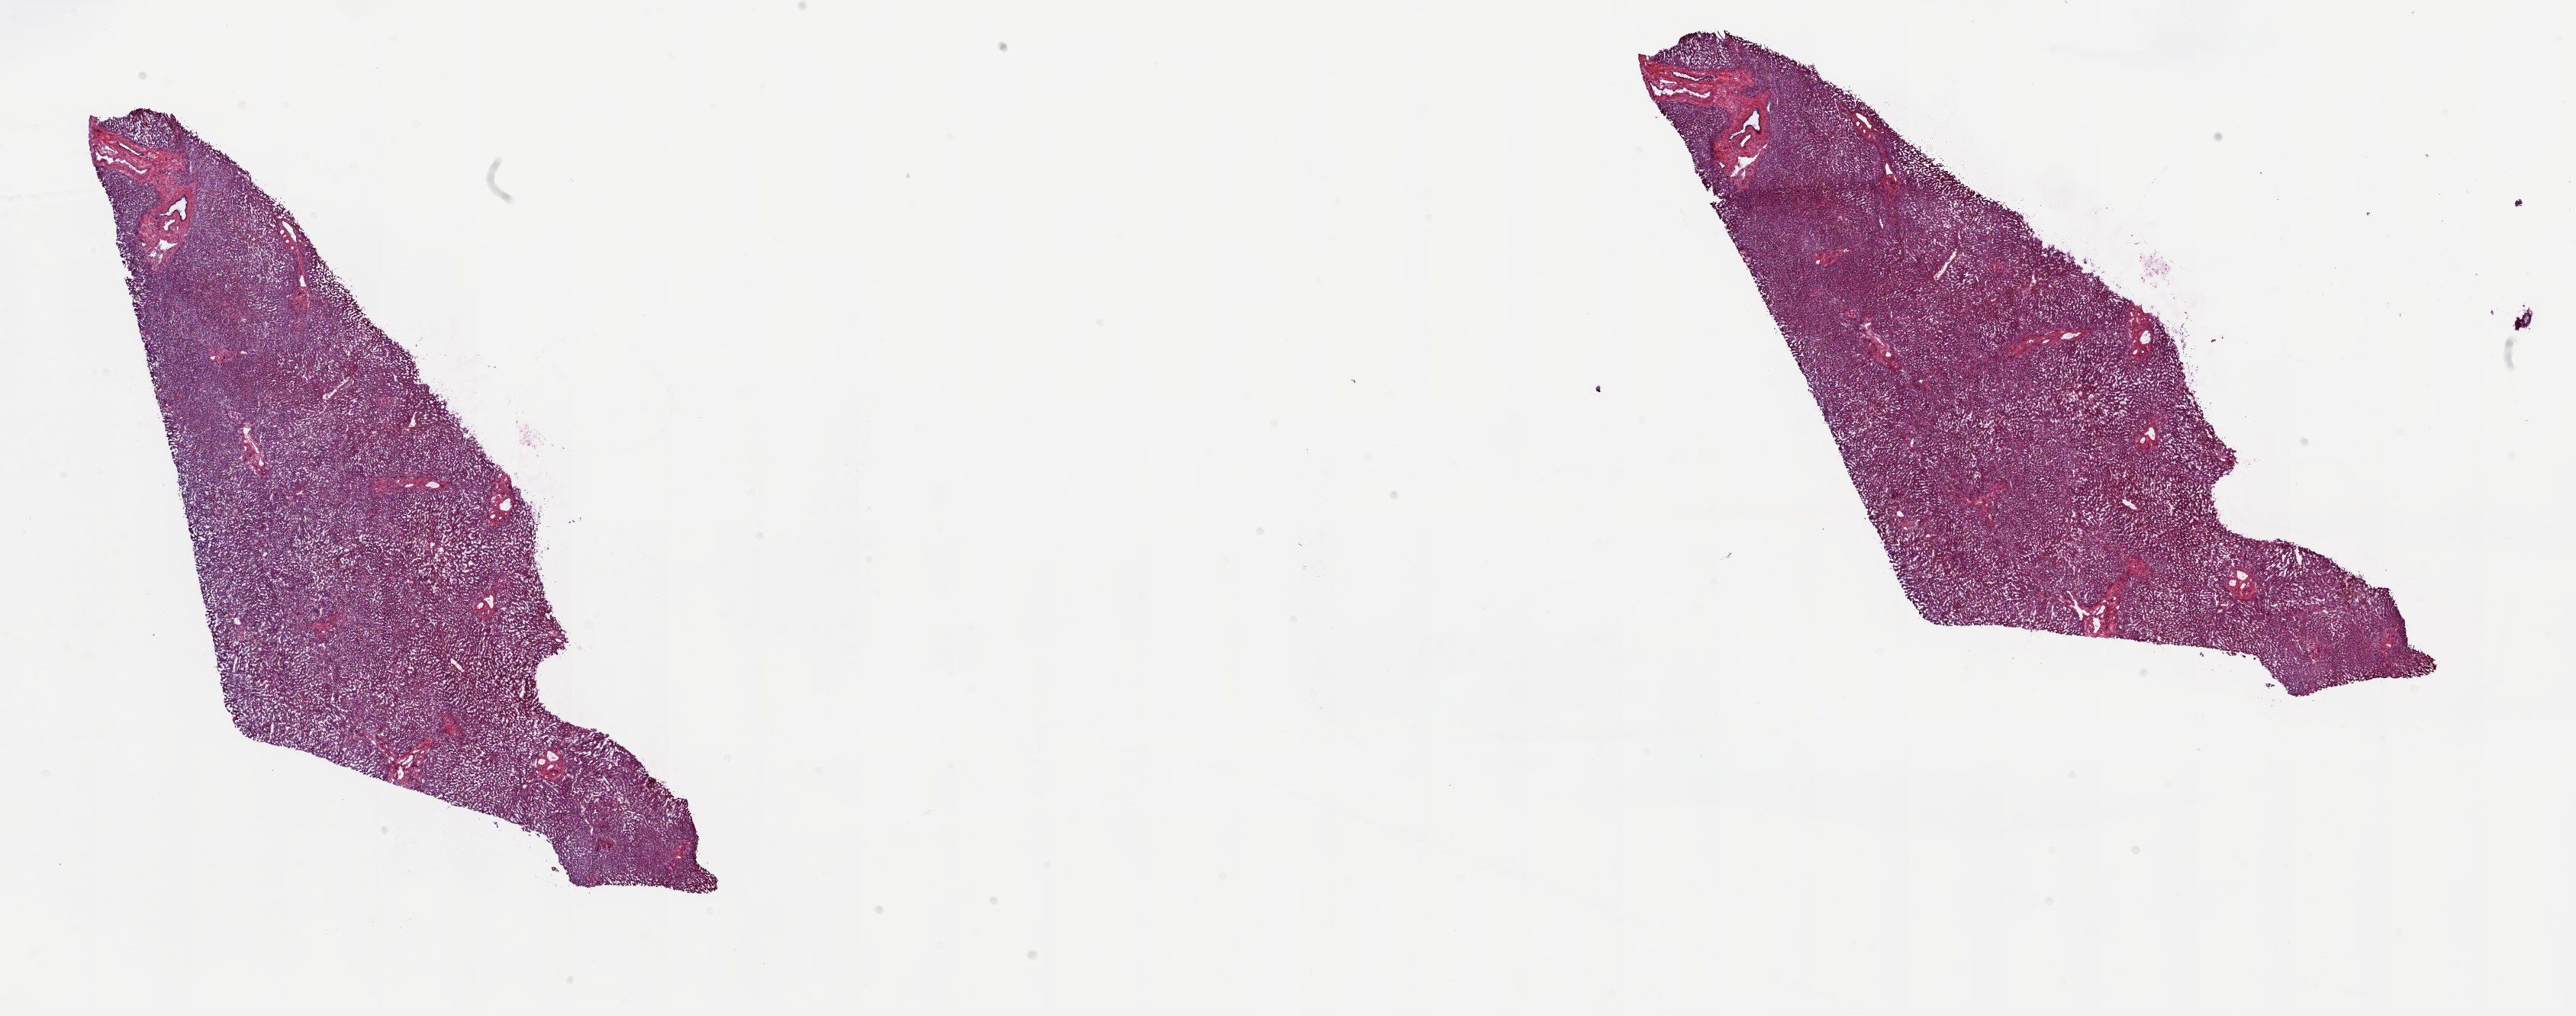
Digitized H&E tissue section (whole slide), a low-resolution overview of the entire scanned area, about 26.8 x 10.6 mm (acquisition: 20x scan); frozen section from the top of the tissue portion; bile duct, solid tissue normal (non-tumour tissue) sample. Female, age 78 years at initial diagnosis. Slide review estimates, as recorded: tumour cells 0%, tumour nuclei 0%, normal cells 100%, stromal cells 0%, necrosis 0%. Infiltration values recorded for this section: lymphocyte infiltration 0%, monocyte infiltration 0%, neutrophil infiltration 0%.
* this section: solid tissue normal (non-tumour) sample from the same patient
* patient diagnosis: Cholangiocarcinoma